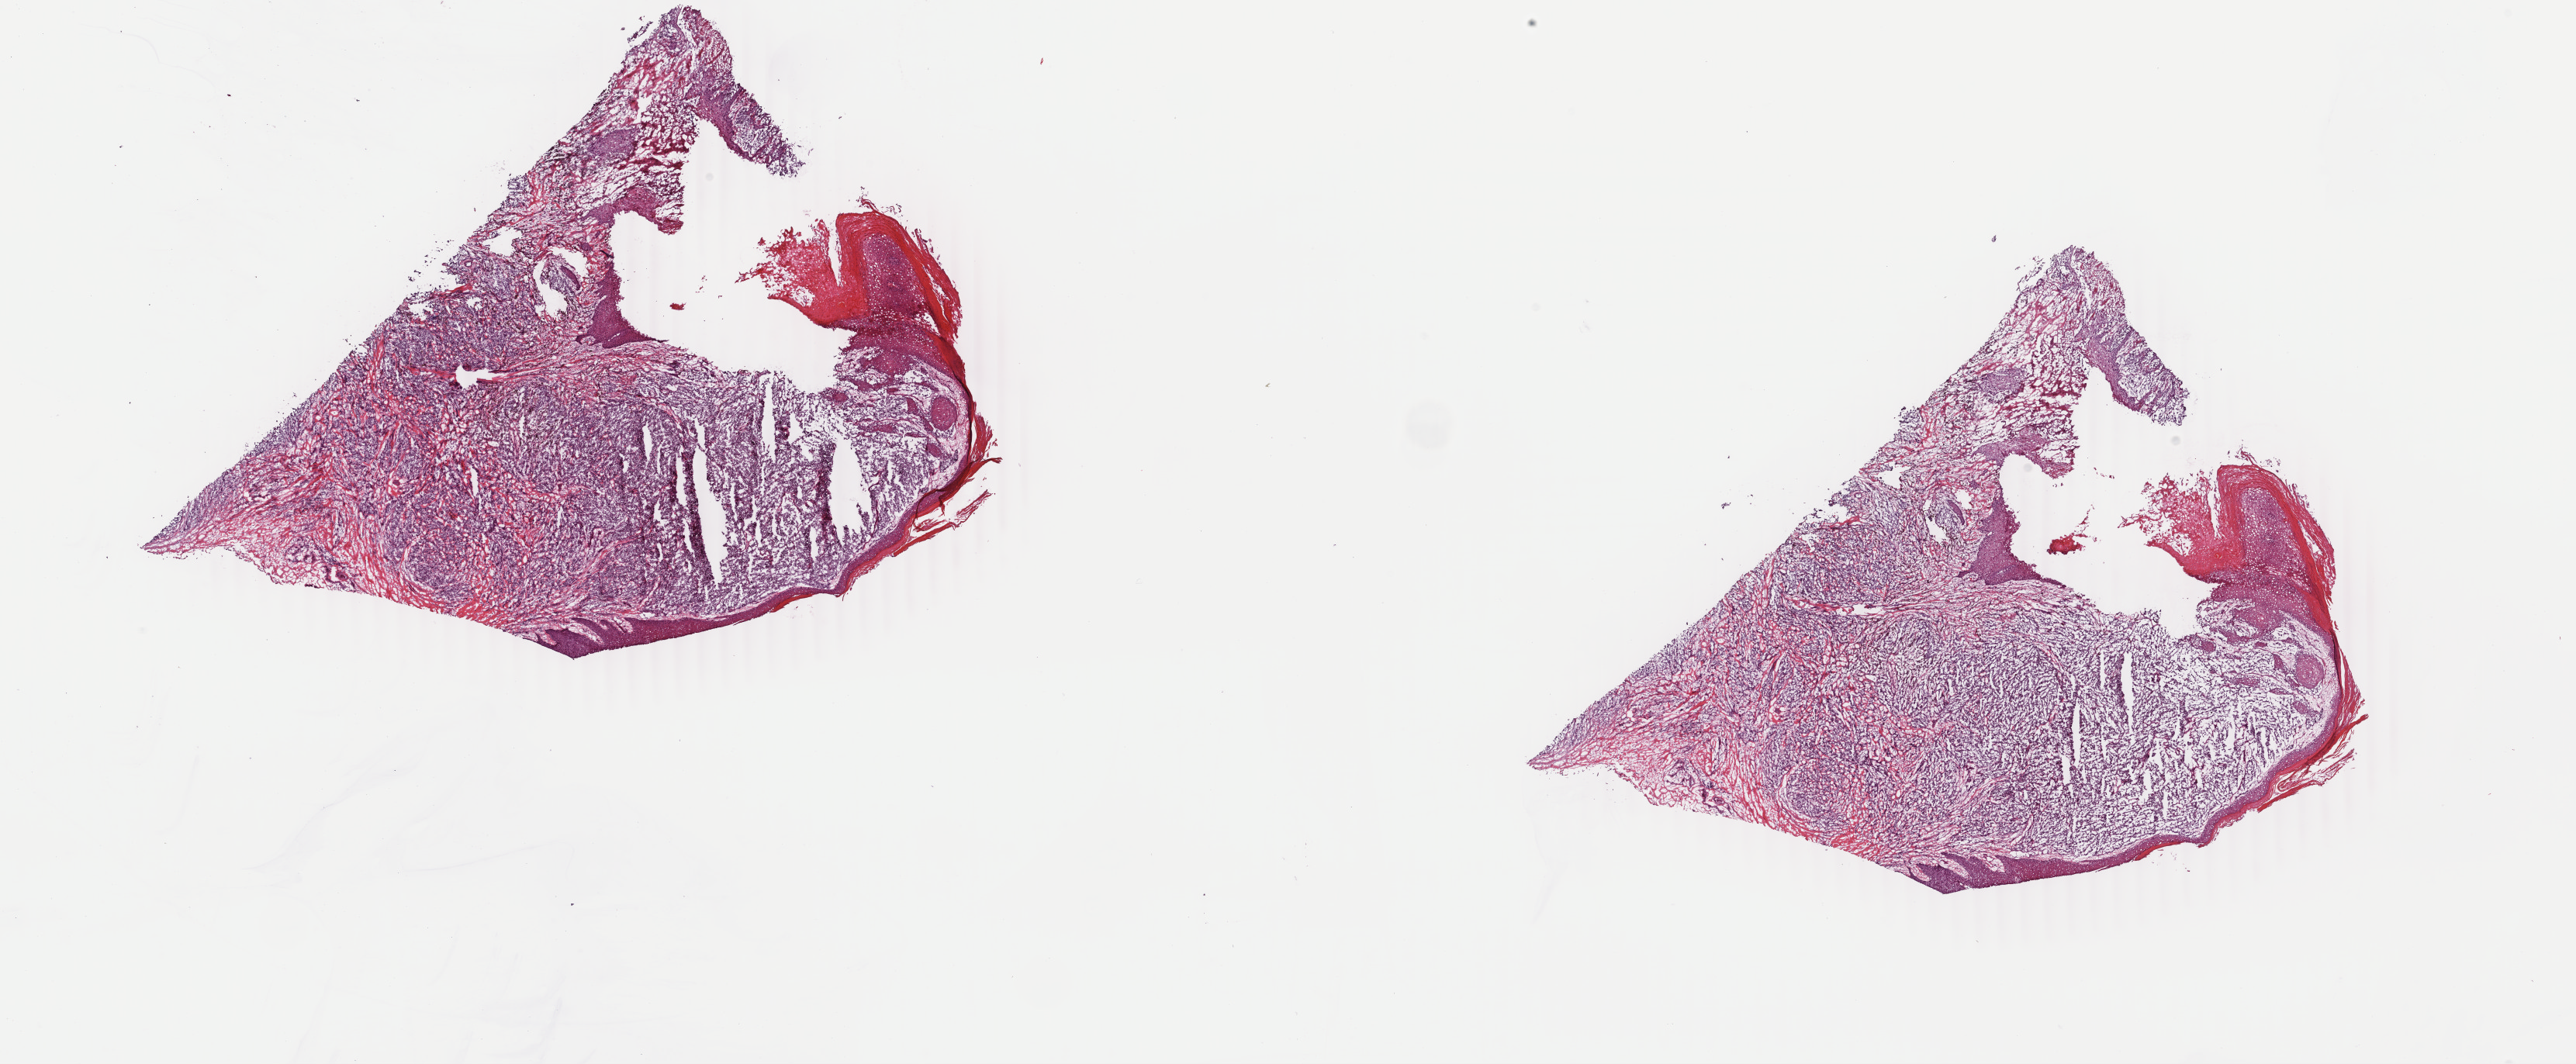
H&E whole-slide image, whole scanned area (about 26.4 x 10.9 mm, from a 40x scan) shown as a low-resolution overview, frozen section from the top of the tissue portion, primary tumour sample from the skin. Female, age 78 years at initial diagnosis. Pathologist review of this section (percent, as recorded): tumour cells 90%, tumour nuclei 88%, normal cells 10%, stromal cells 0%, necrosis 0%. Inflammatory infiltration, as recorded: lymphocyte infiltration 0%, monocyte infiltration 0%, neutrophil infiltration 0%.
TNM: T4b NX M0. Pathologic diagnosis: Nodular melanoma. AJCC pathologic stage: IIC (7th edition).